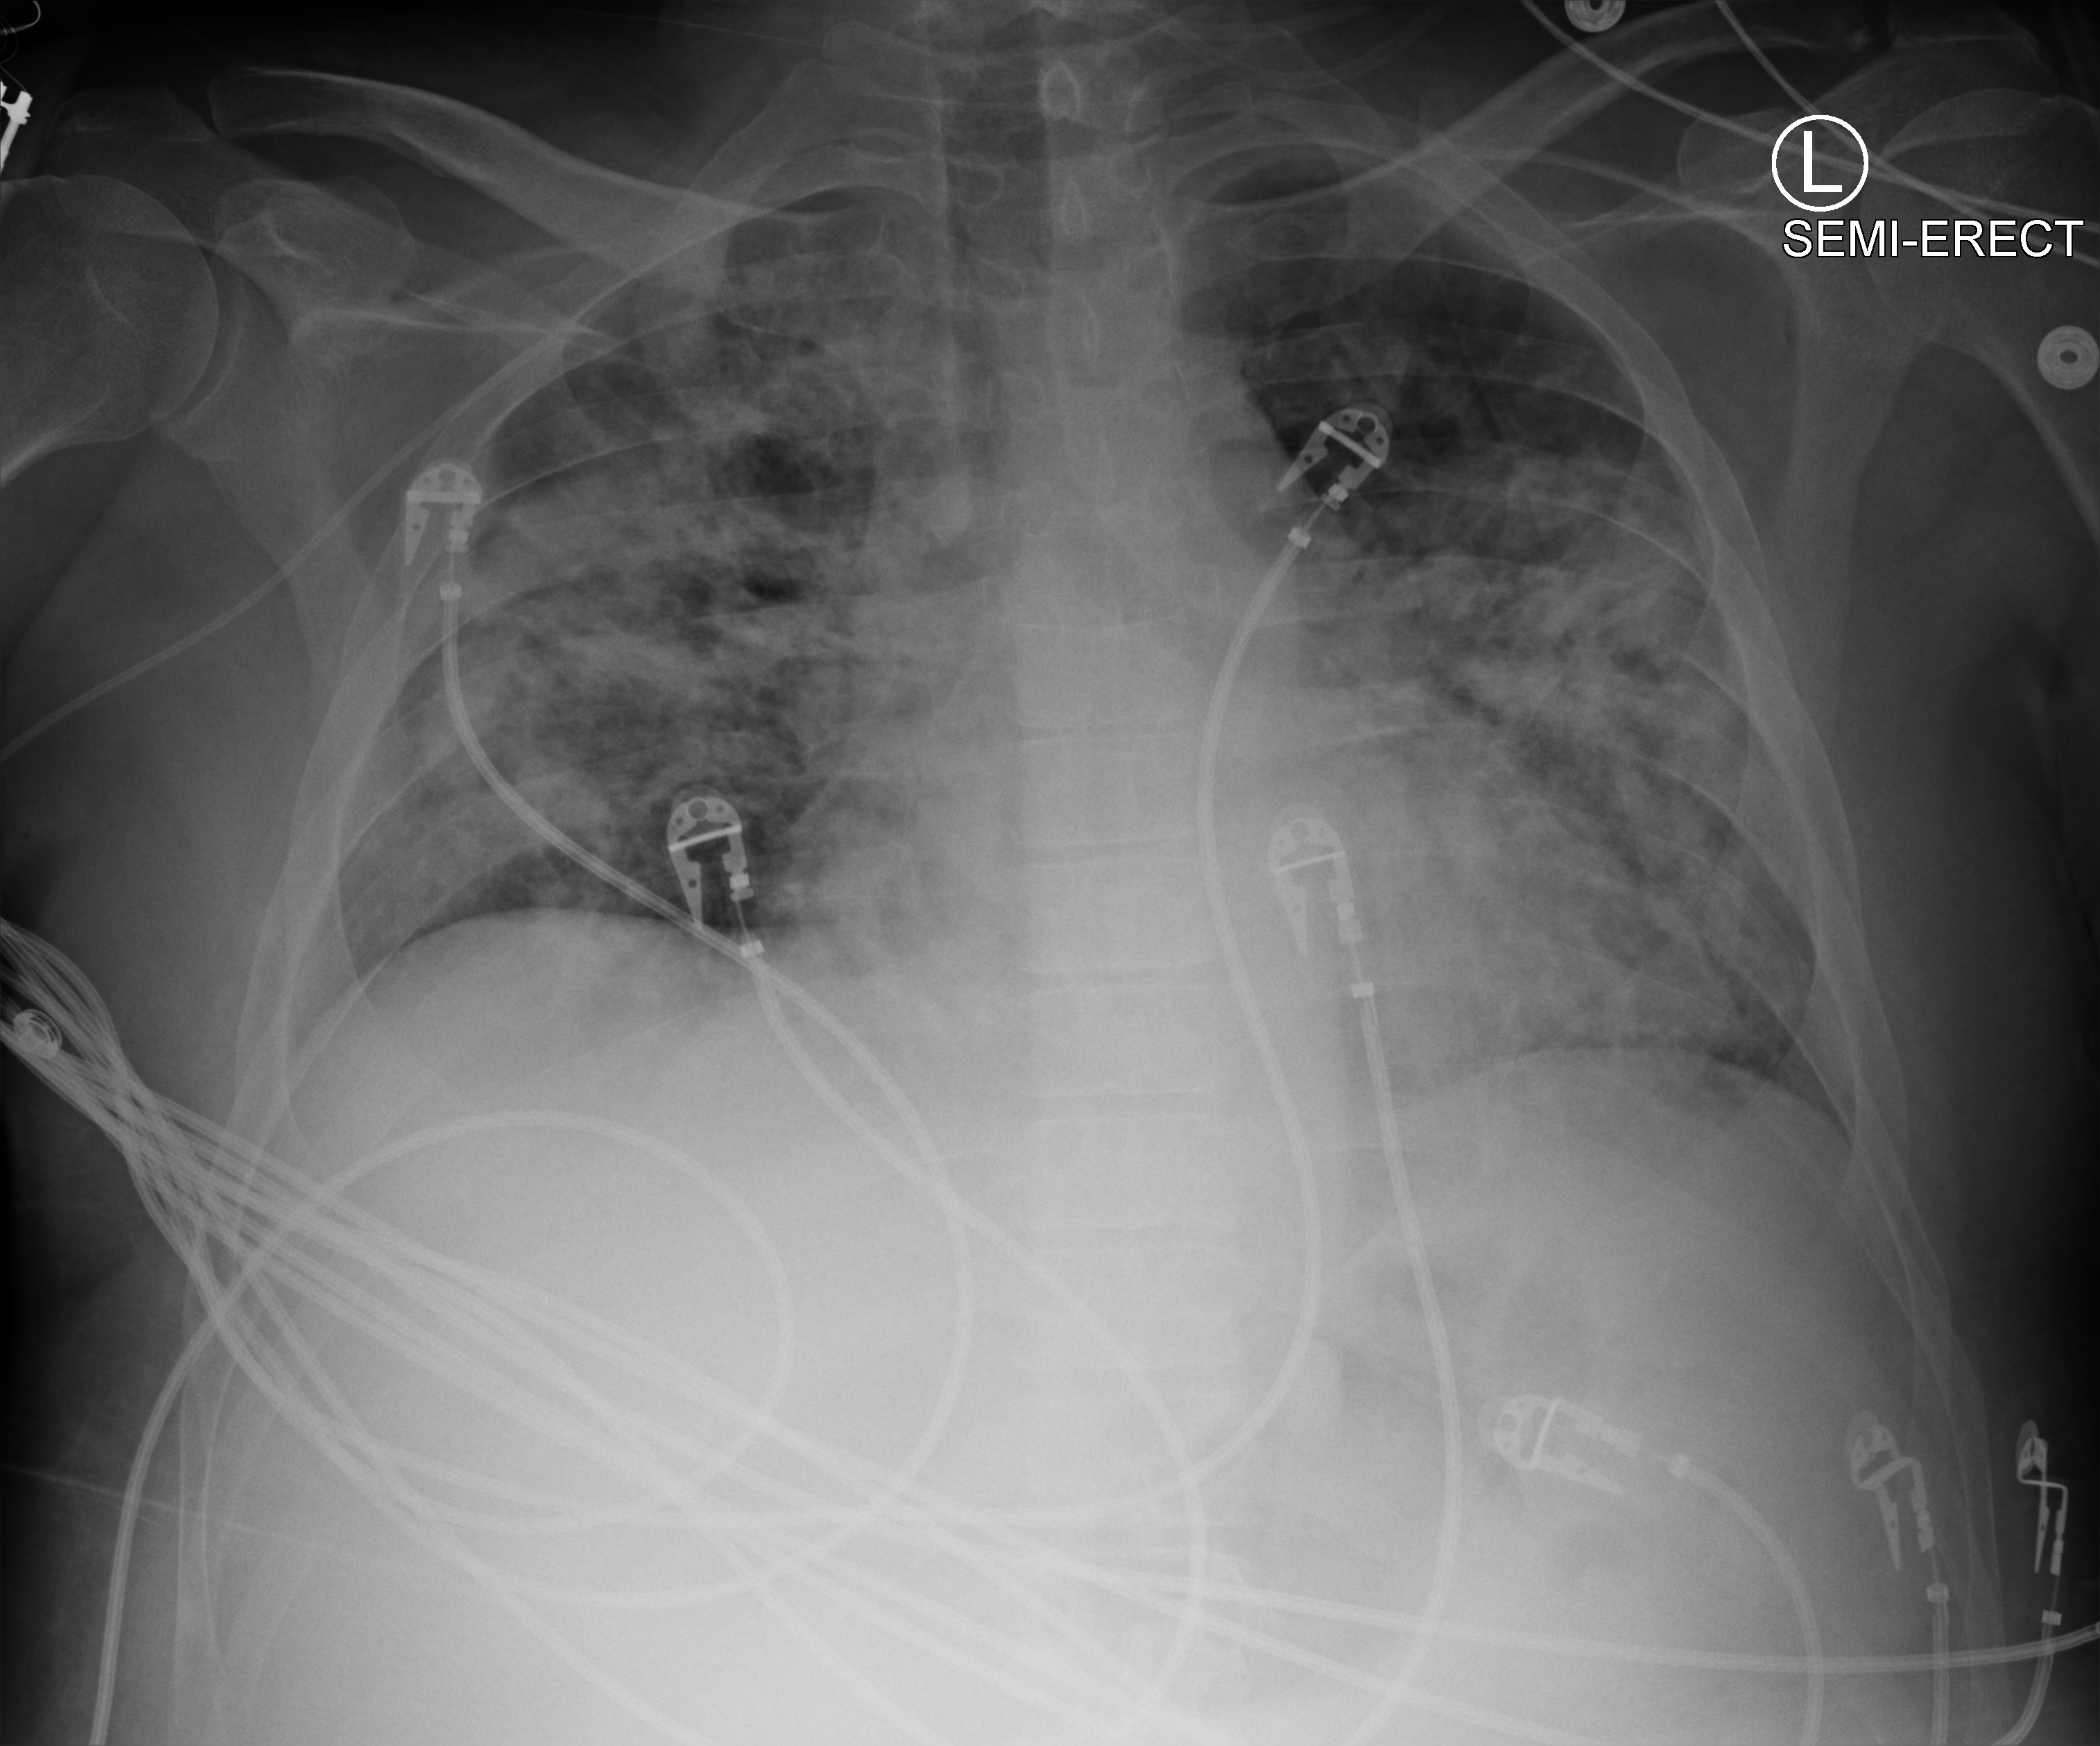
Portable chest radiograph, anteroposterior (AP) projection. Male patient hospitalised with COVID-19, age 18–59 years.
From the hospital-stay record, not from the radiograph (when in the stay this image was taken is not recorded): mechanically ventilated during this hospital stay: yes; admitted to intensive care during this hospital stay: yes; length of hospital stay: 20 days.